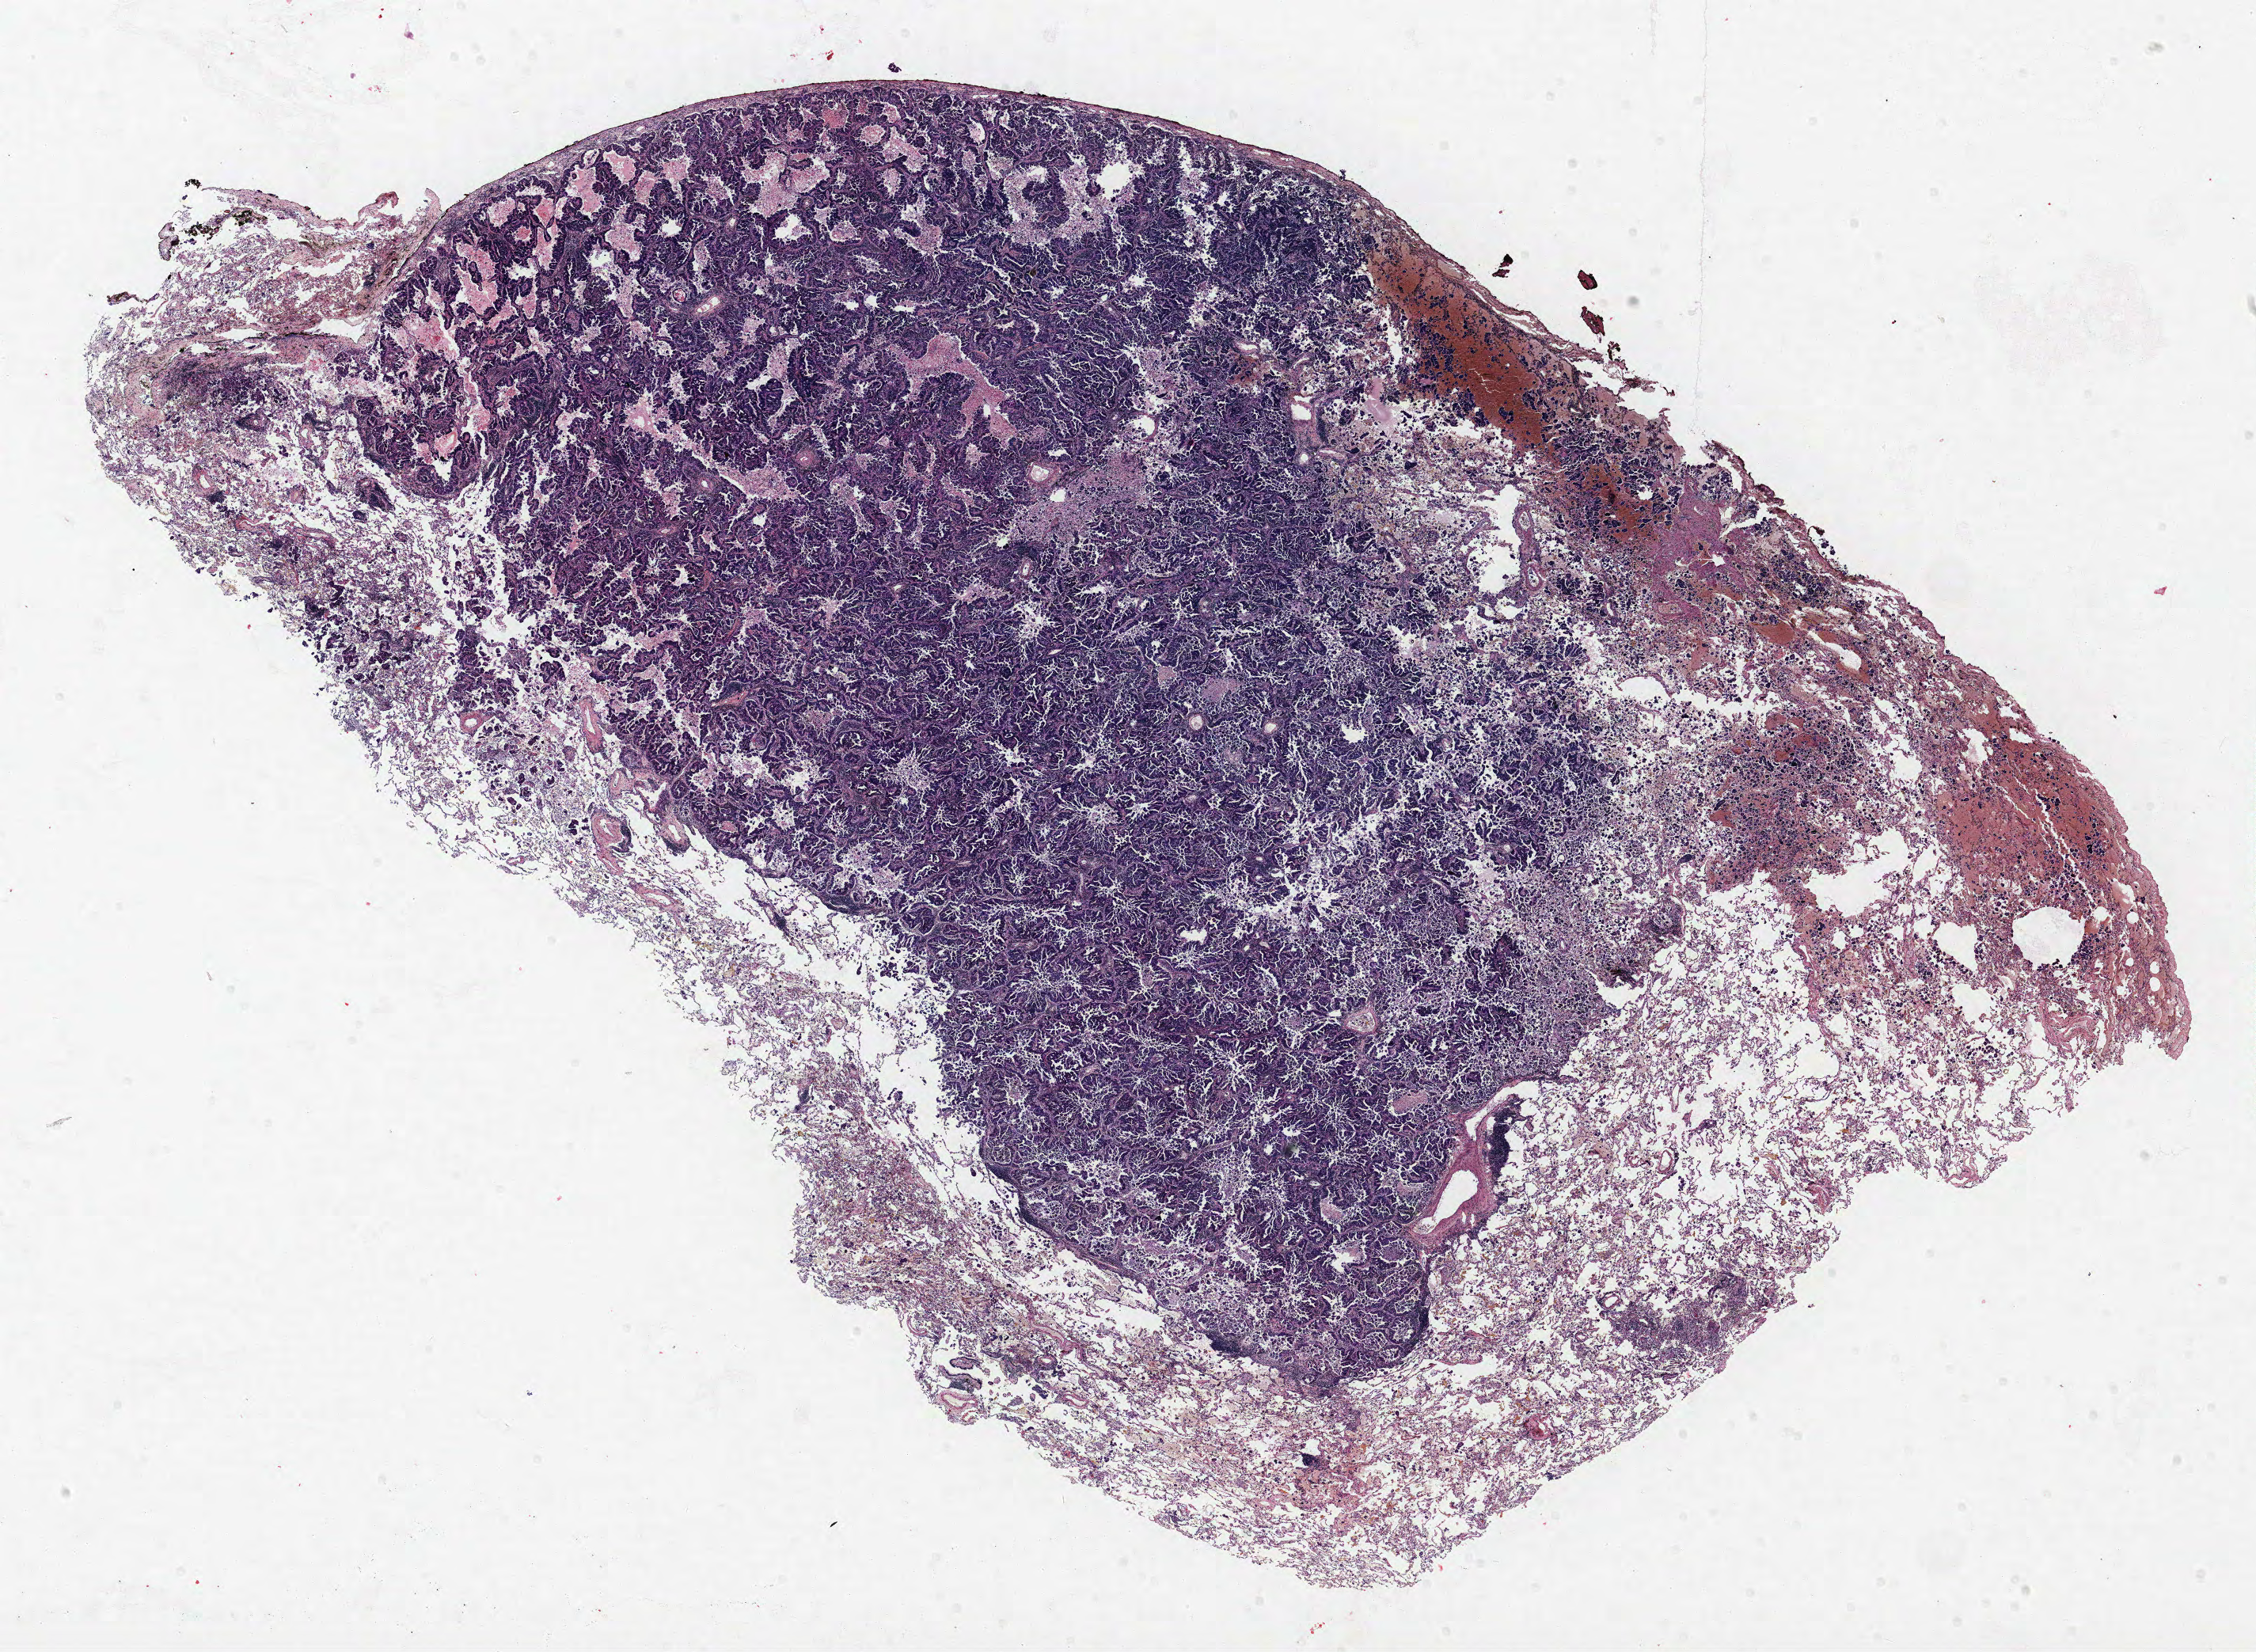
H&E whole-slide image — low-resolution overview of the scanned area, about 22.8 x 16.7 mm (acquisition: 40x scan); formalin-fixed paraffin-embedded (FFPE) section; lung. Male, age 69 at enrolment. Former smoker at enrolment. Grade: moderately differentiated (G2).
• tumour size (pathology): 23 mm
• stage (AJCC 6th edition): IA
• ICD-O-3 topography: upper lobe of lung (C34.1)
• primary tumour location (clinical record): right upper lobe
• participant's lung-cancer diagnosis: Adenocarcinoma, NOS